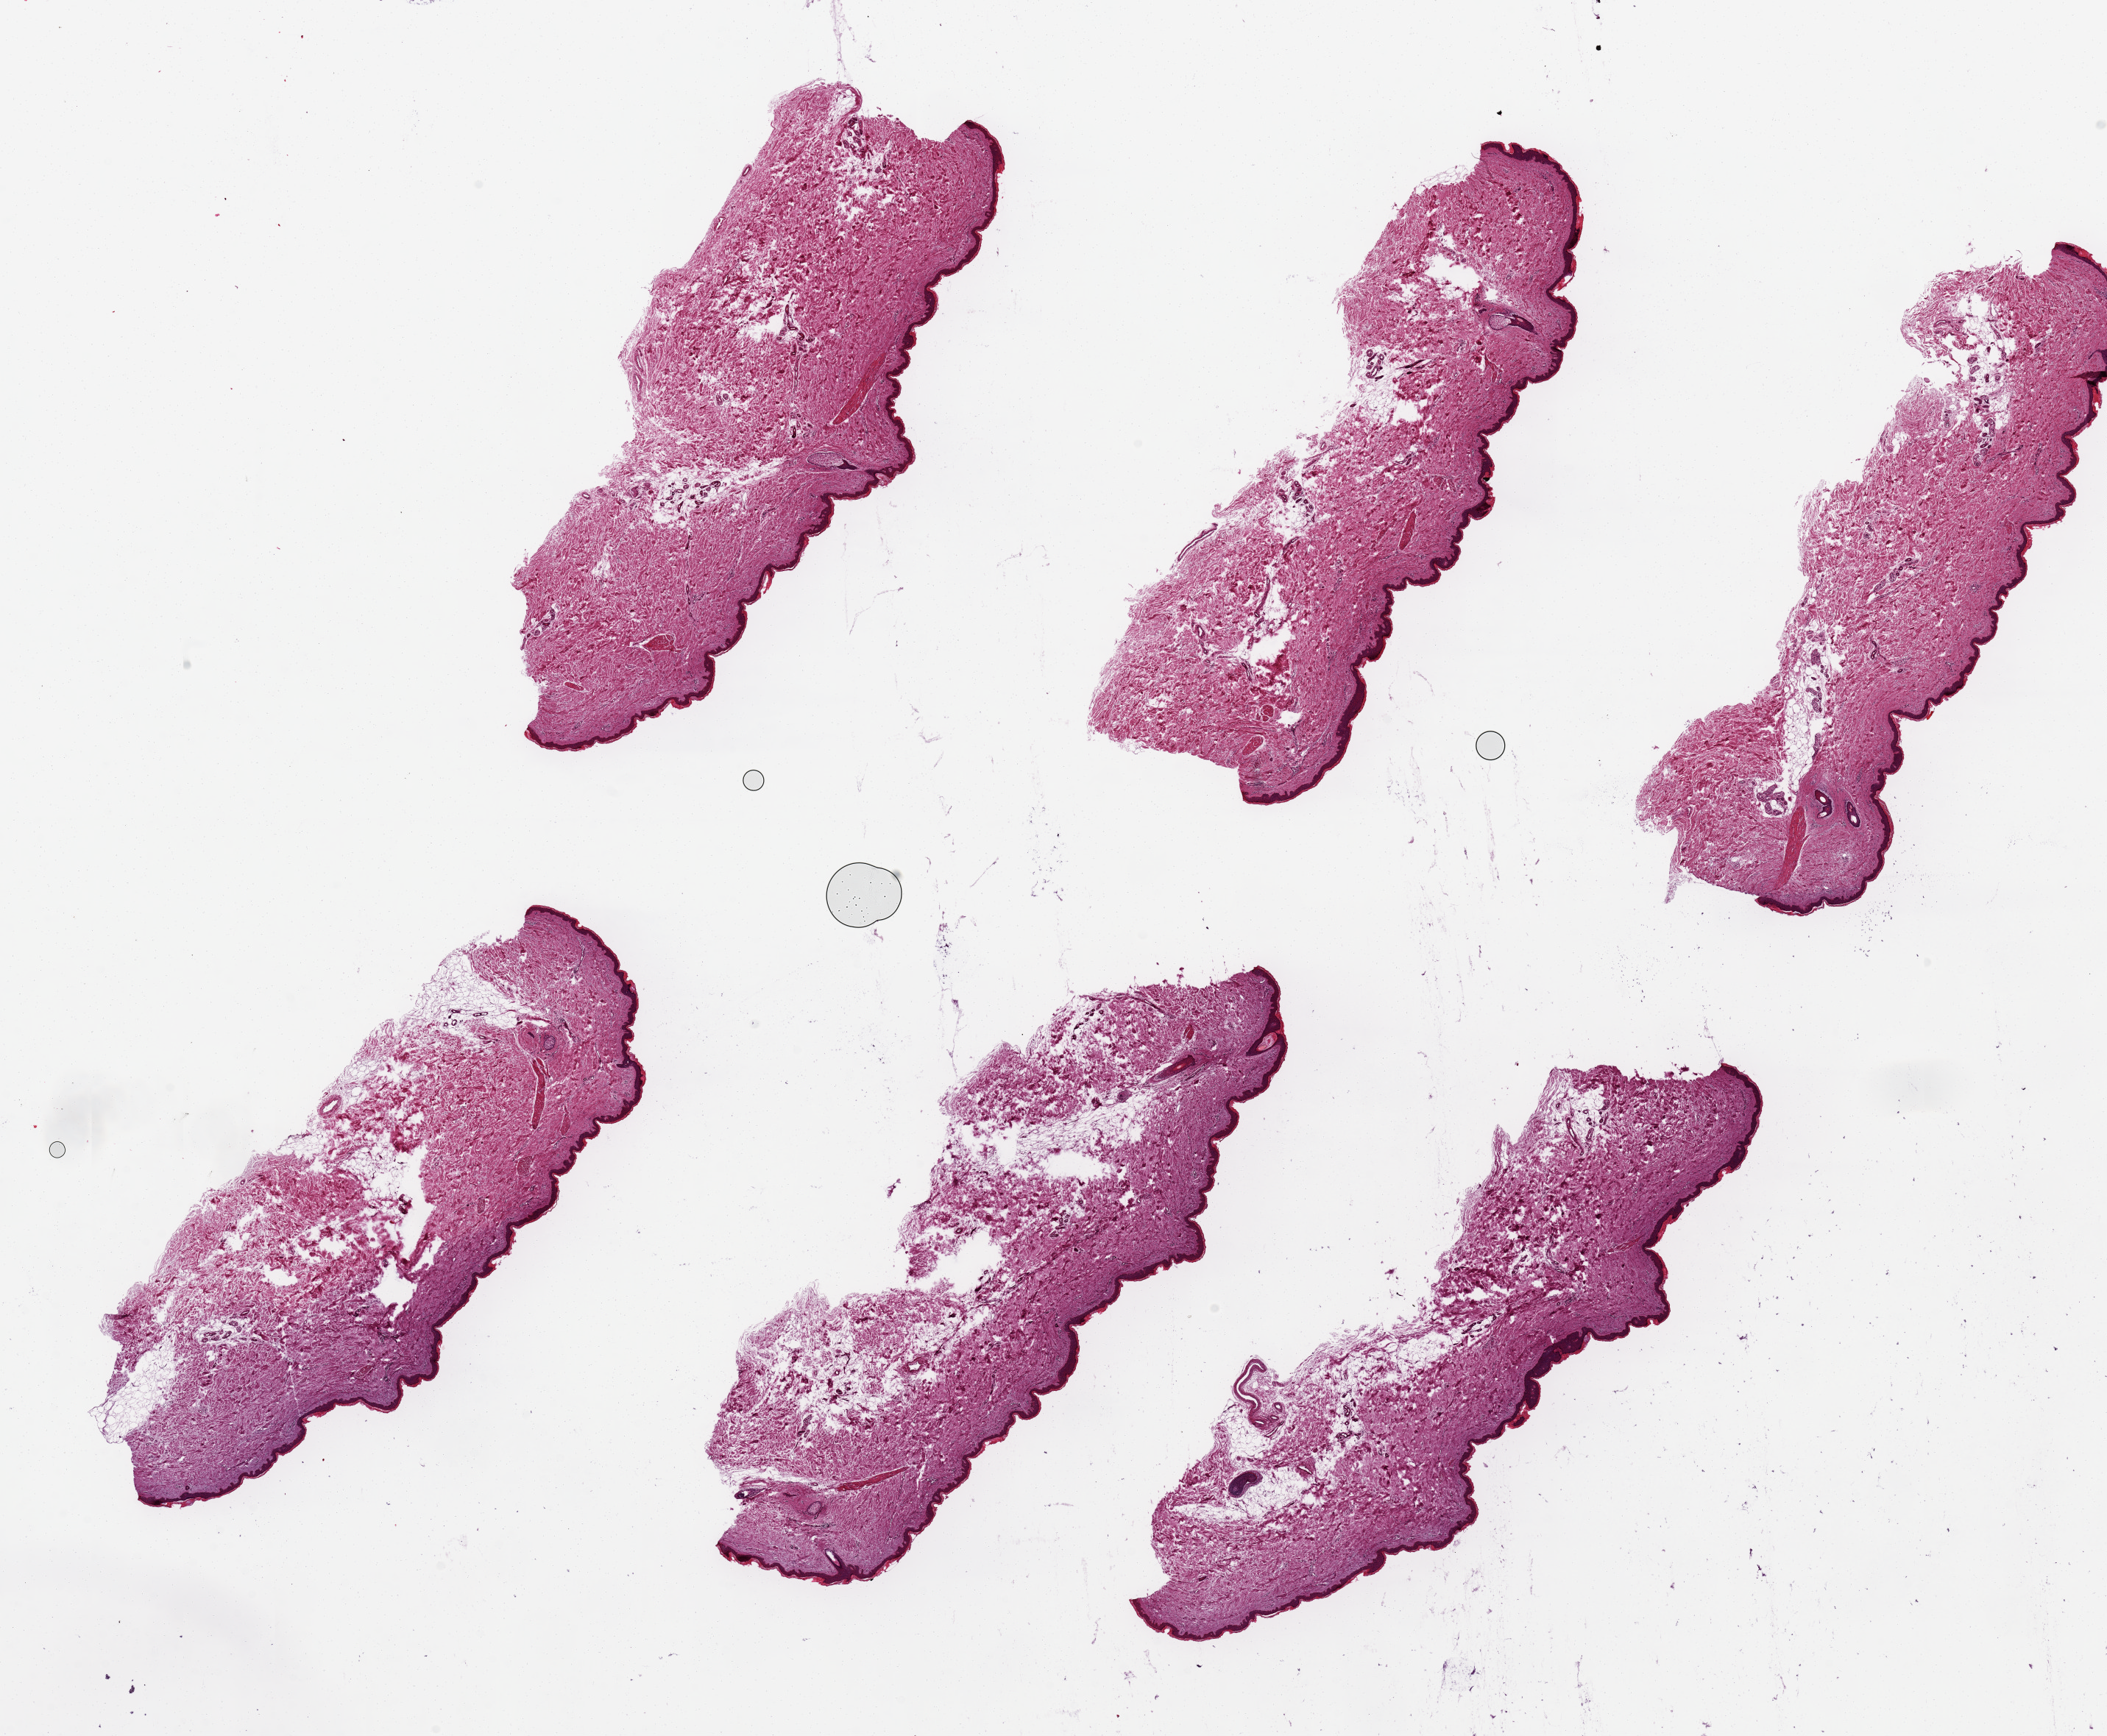
Digitized hematoxylin and eosin (H&E)-stained section — whole scanned area (about 22.6 x 18.7 mm) shown as a low-resolution overview. PAXgene-fixed, paraffin-embedded tissue. Section of skin of lower leg (target tissue). Donor tissue sample. Donor: female.
Review note (as recorded): 6 pieces ~8x2mm. Squamous epithelium is 2-3% of thickness.